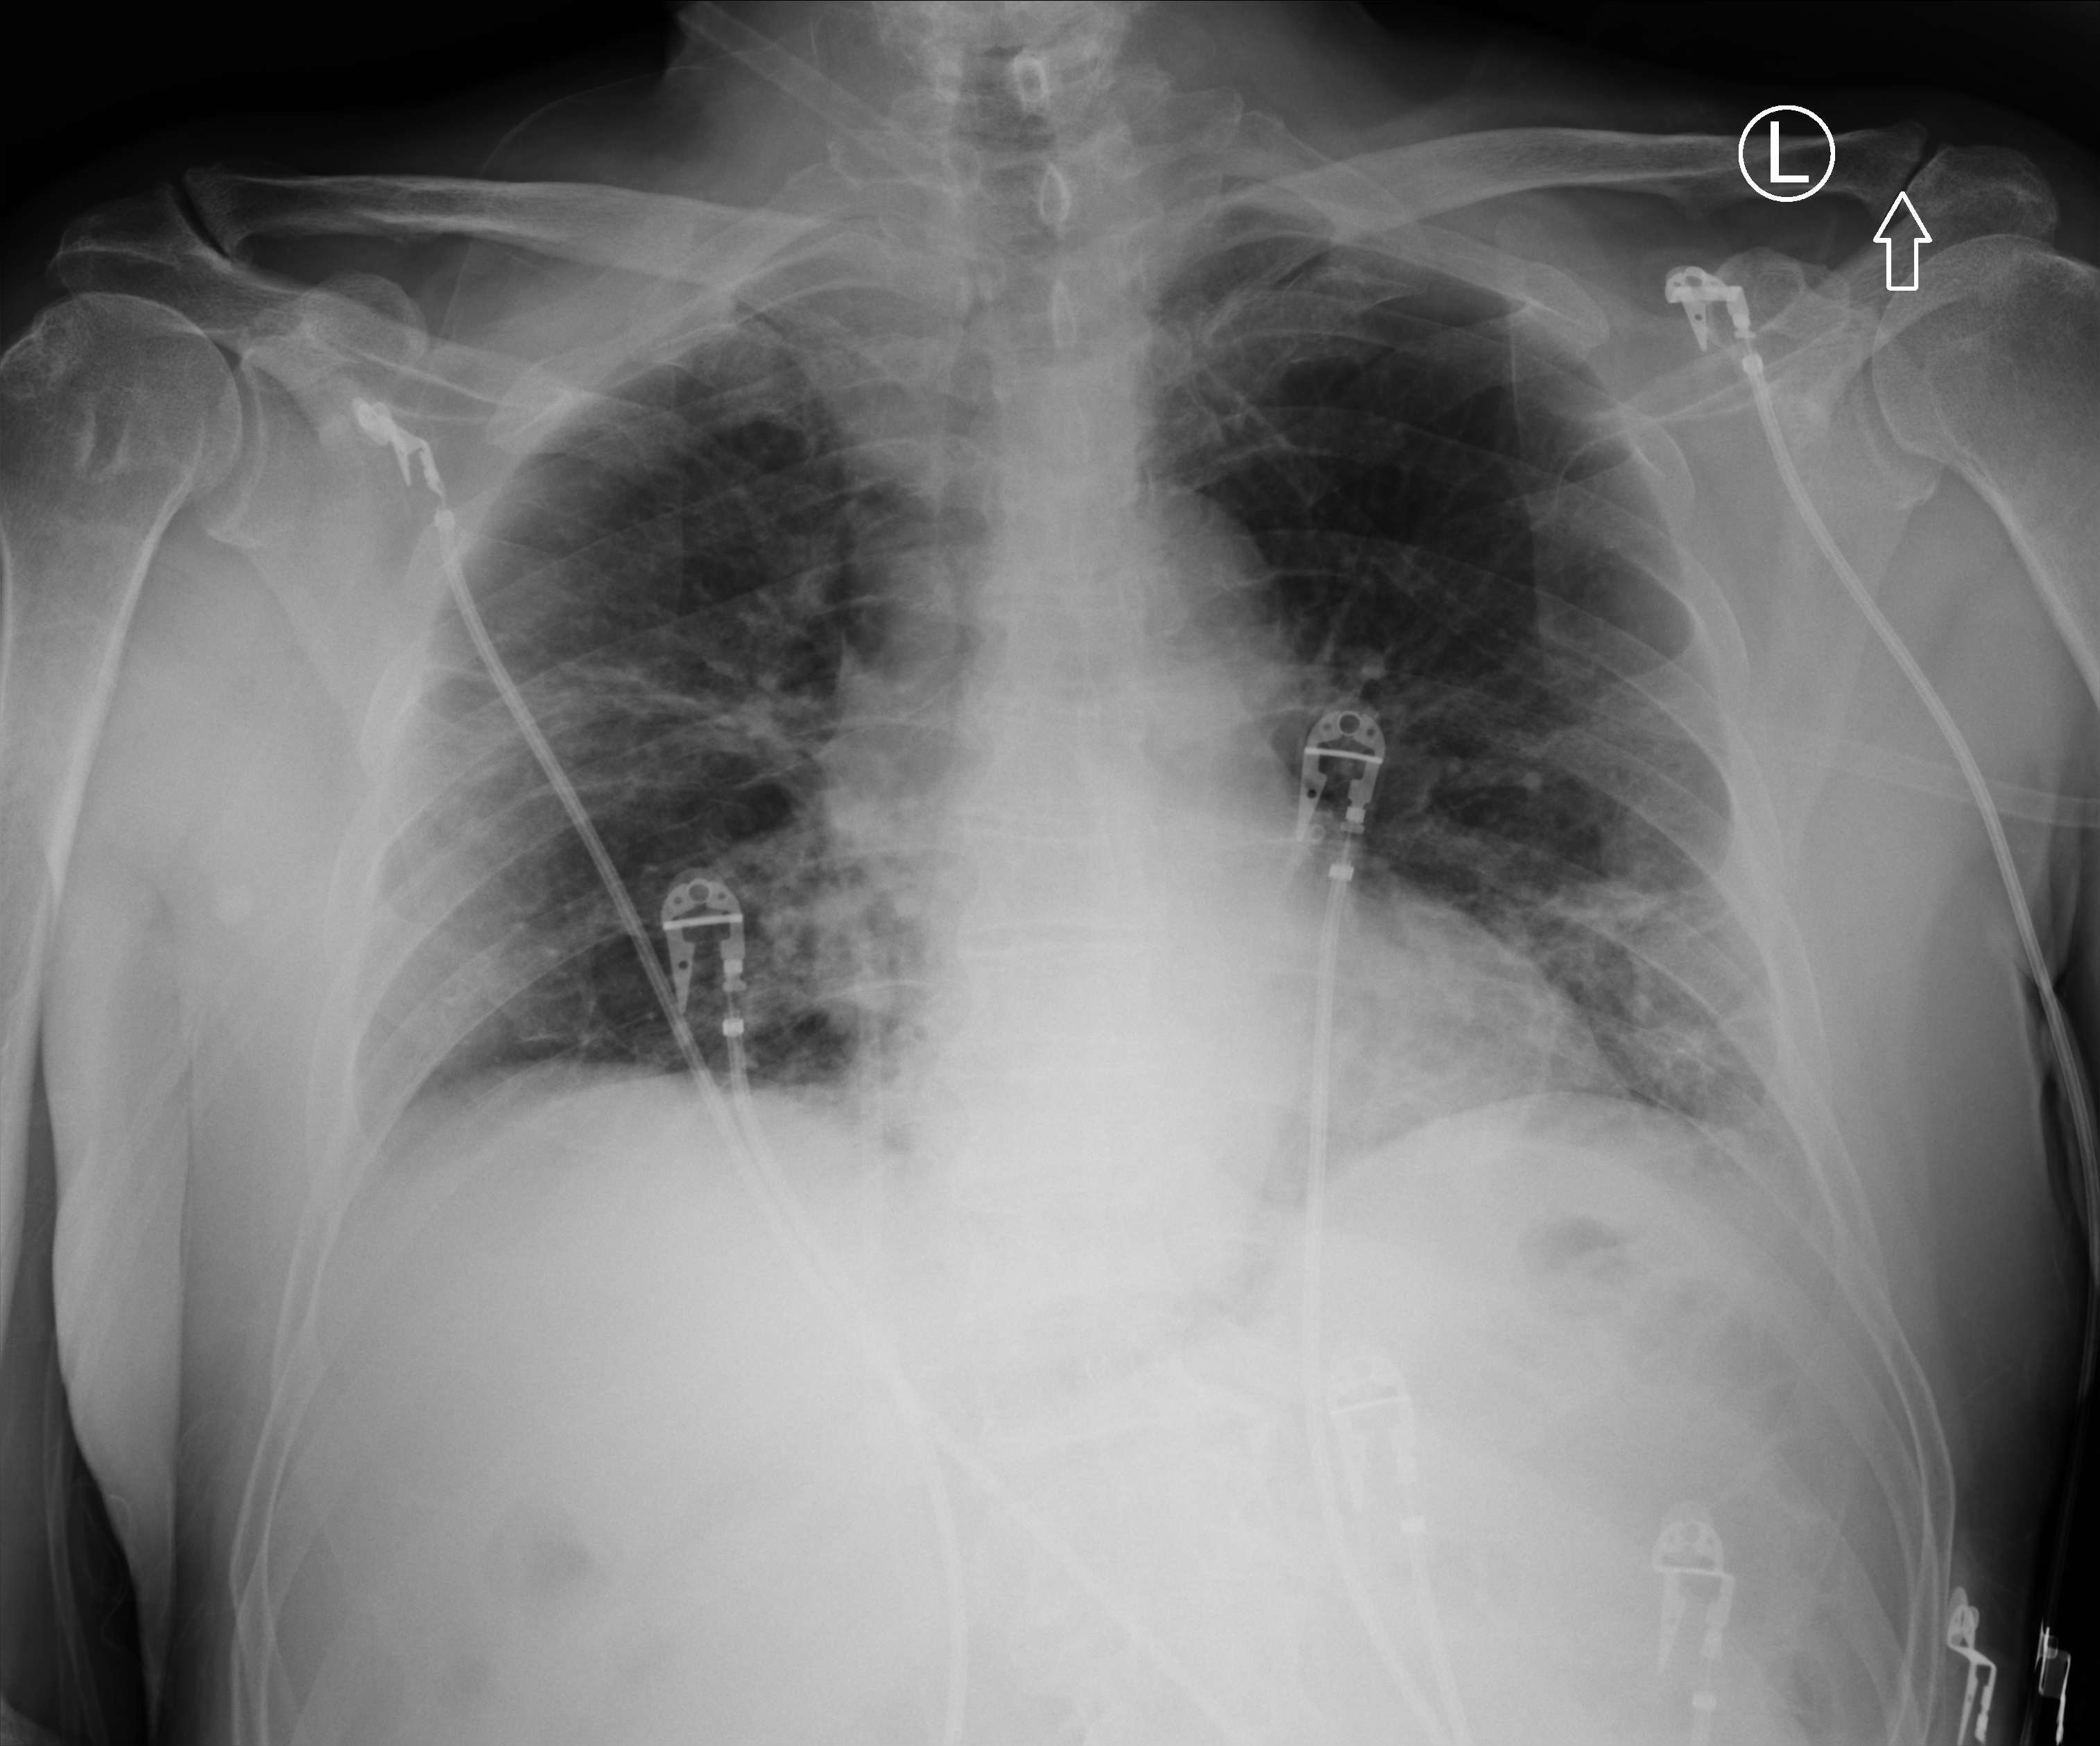
Chest X-ray (portable). Male patient hospitalised with COVID-19, age 60–74 years.
From the hospital-stay record, not from the radiograph (when in the stay this image was taken is not recorded):
- hypertension (admission record): yes
- mechanically ventilated during this hospital stay: no
- smoking status (admission record): former